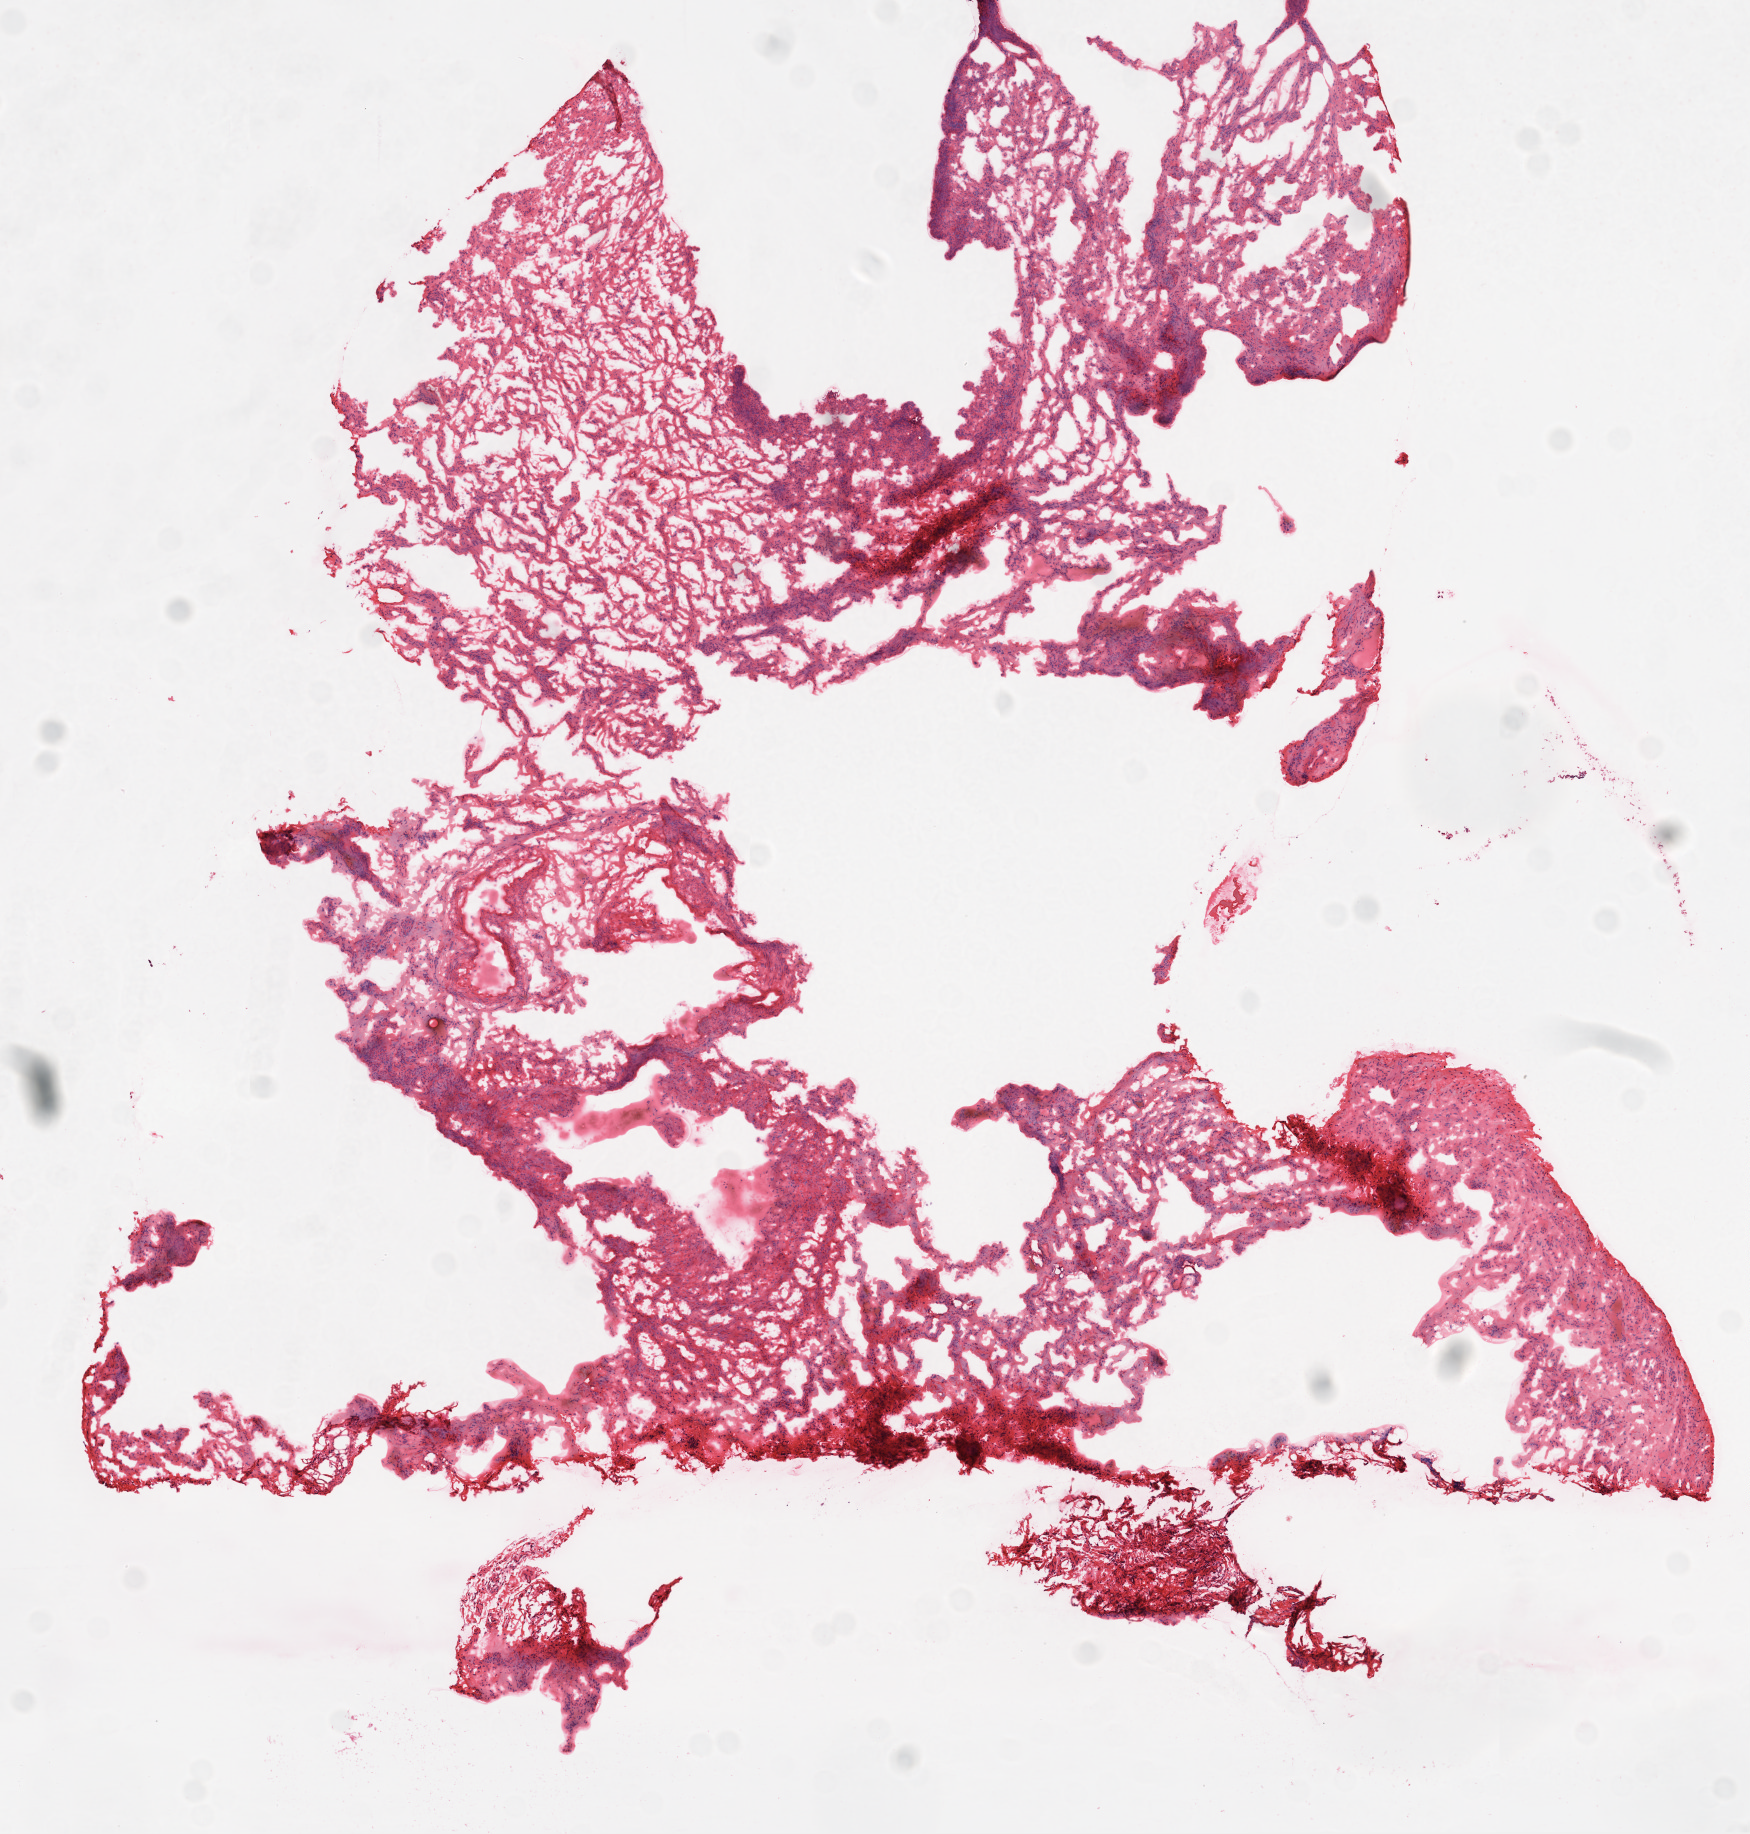
Whole-slide histology image, H&E-stained — shown as a low-resolution overview of the whole scanned area (about 7.0 x 7.4 mm), frozen section from the top of the tissue portion, ovary, solid tissue normal (non-tumour tissue) sample. Female patient; age at initial diagnosis 56 years.
This section: solid tissue normal (non-tumour) sample from the same patient. Patient diagnosis: Serous cystadenocarcinoma, NOS.